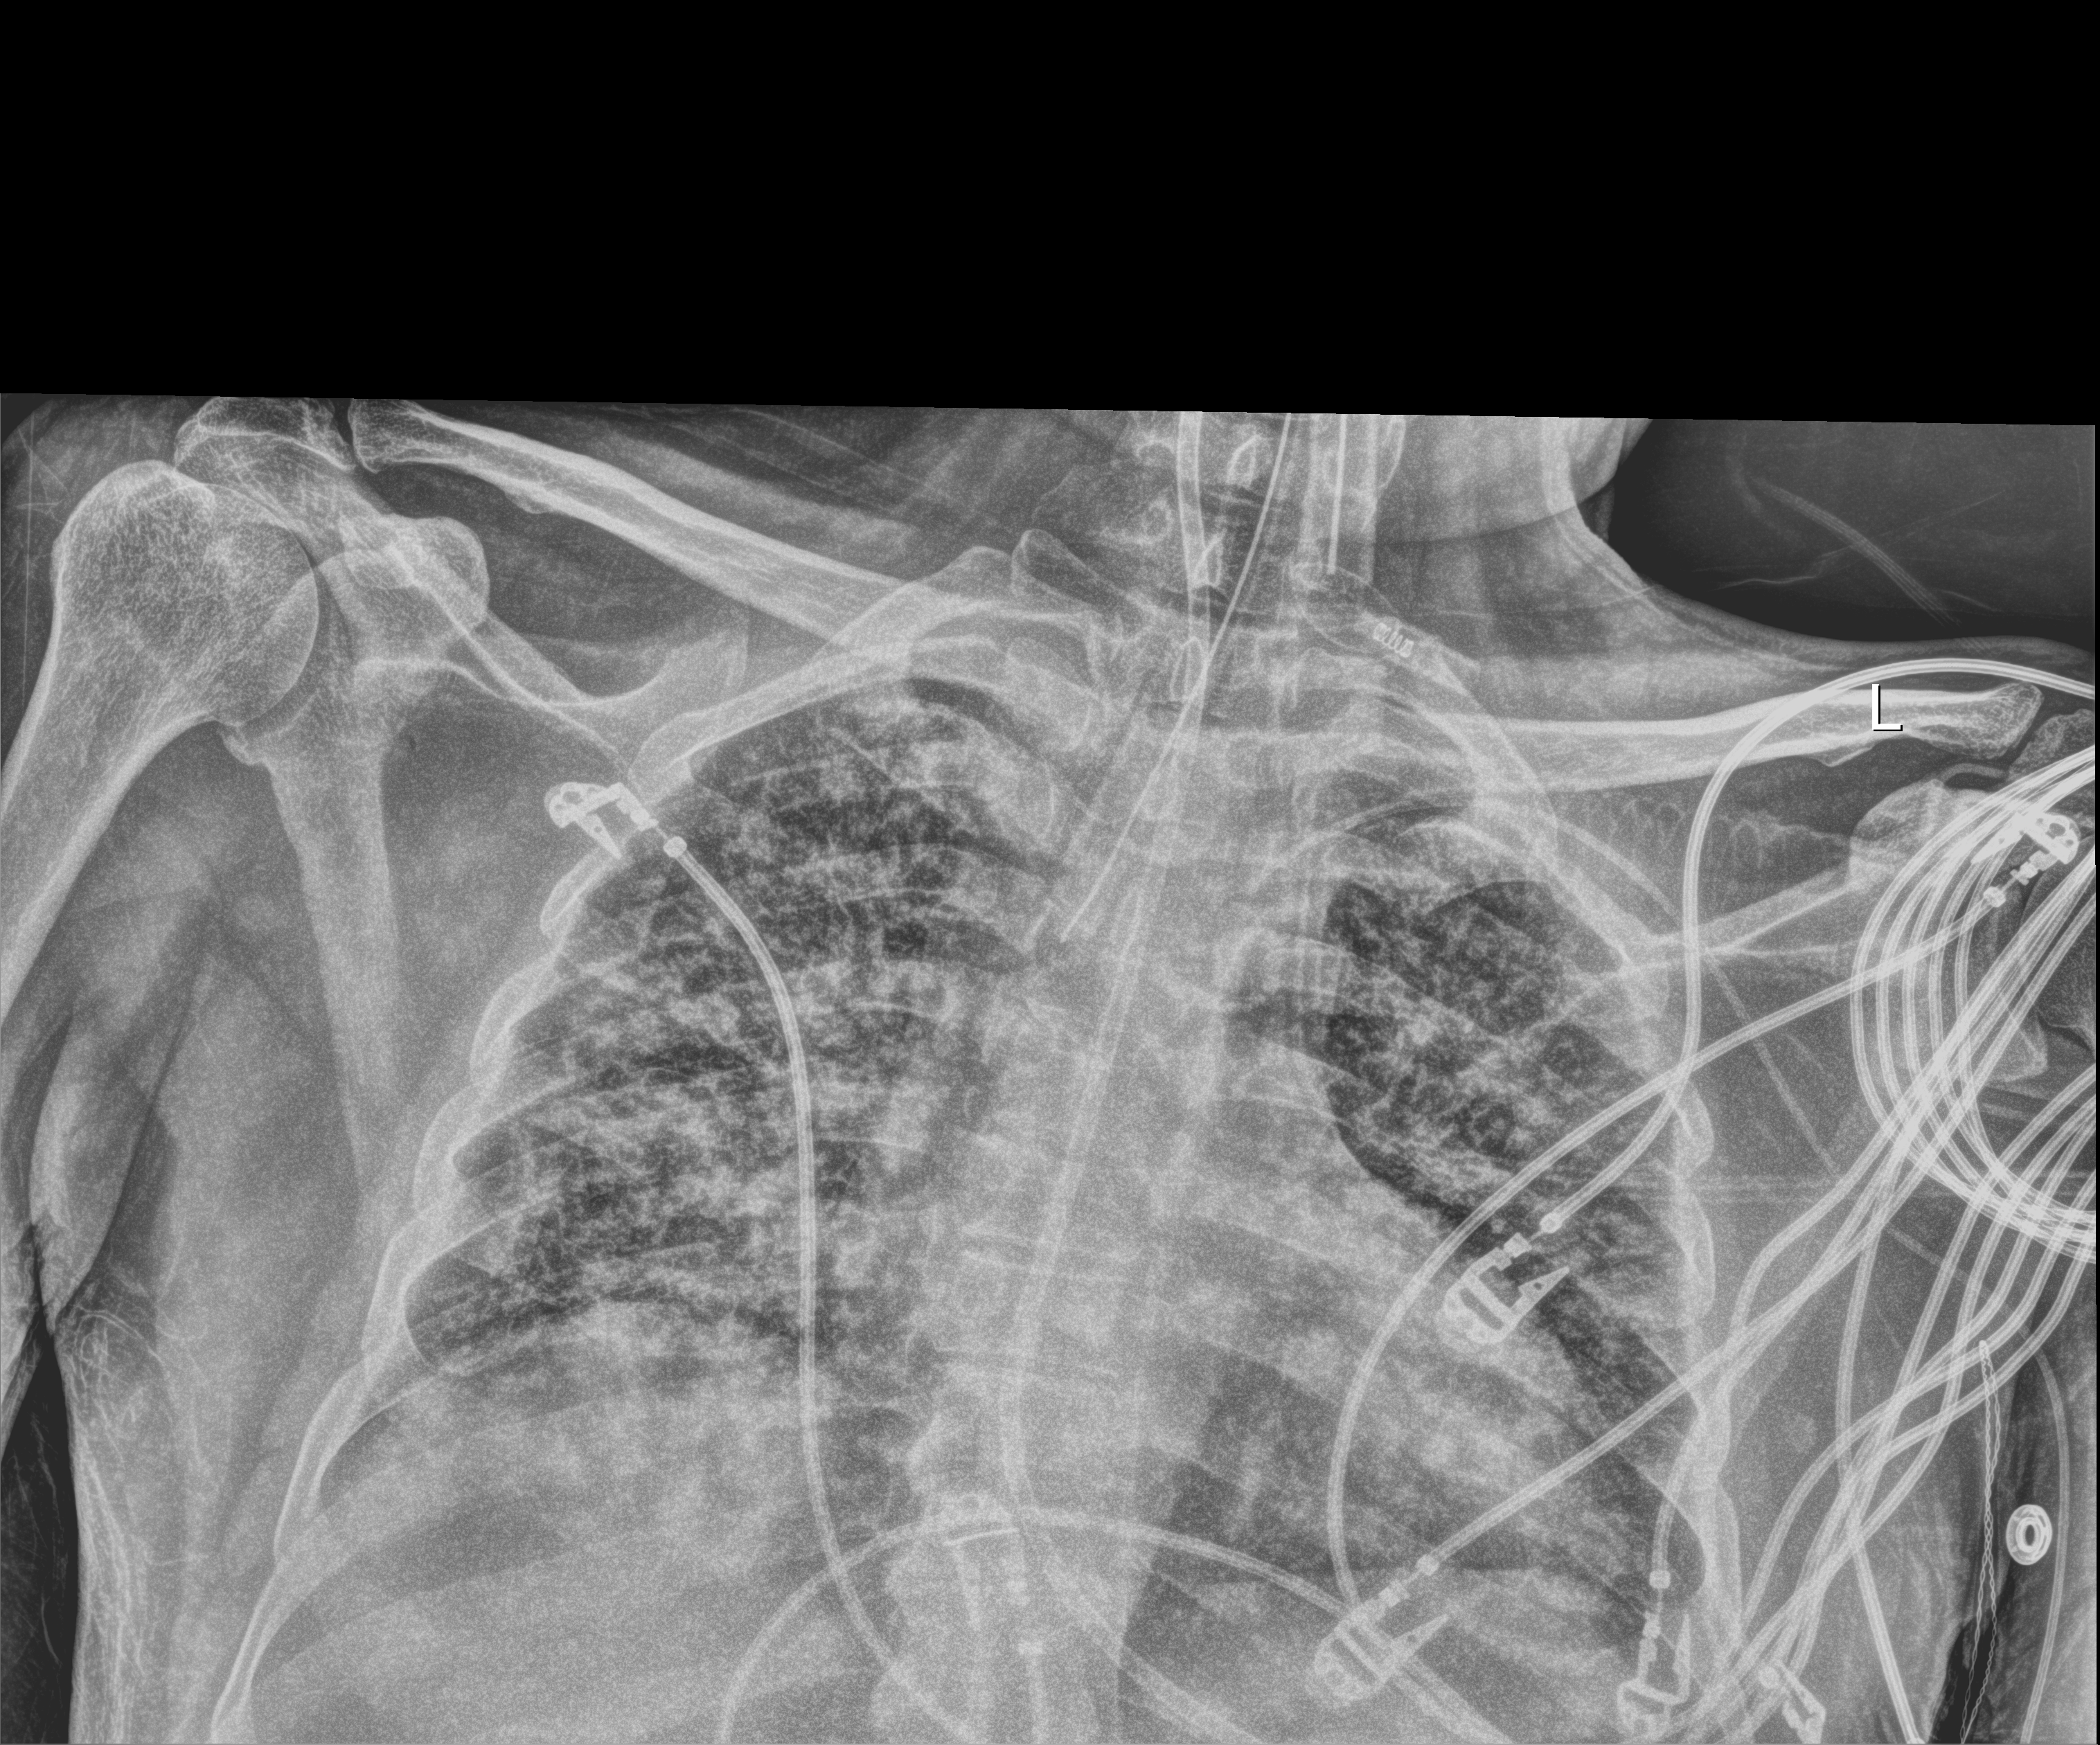
Bedside chest radiograph (digital radiography), anteroposterior (AP) projection. Patient hospitalised with COVID-19; male, aged 18–59 years.
Hospital-stay facts (about this admission, not read from this image; timing relative to this image not recorded): diabetes (admission record): no.